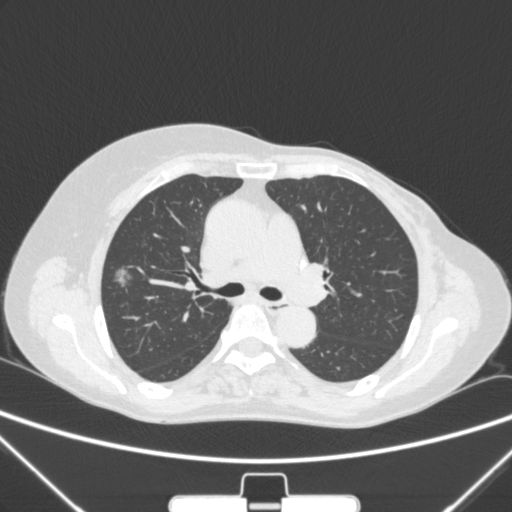
Chest CT, one axial slice. Position 161 of 265 along the scan axis. 120 kVp. Lung window (W 1500 / L -600 HU). 1 mm slice thickness. 512 × 512 image matrix. Female patient, age 64 years. Case-level facts recorded for this patient, not image findings: clinical TNM (as recorded): T1c N0 M0; histopathological grade: G1-2.
Outlined on this slice (rectangle marked by the reading radiologist):
- lung tumour (recorded histology: adenocarcinoma): bounding box [x1, y1, x2, y2] px = [106, 259, 134, 299]